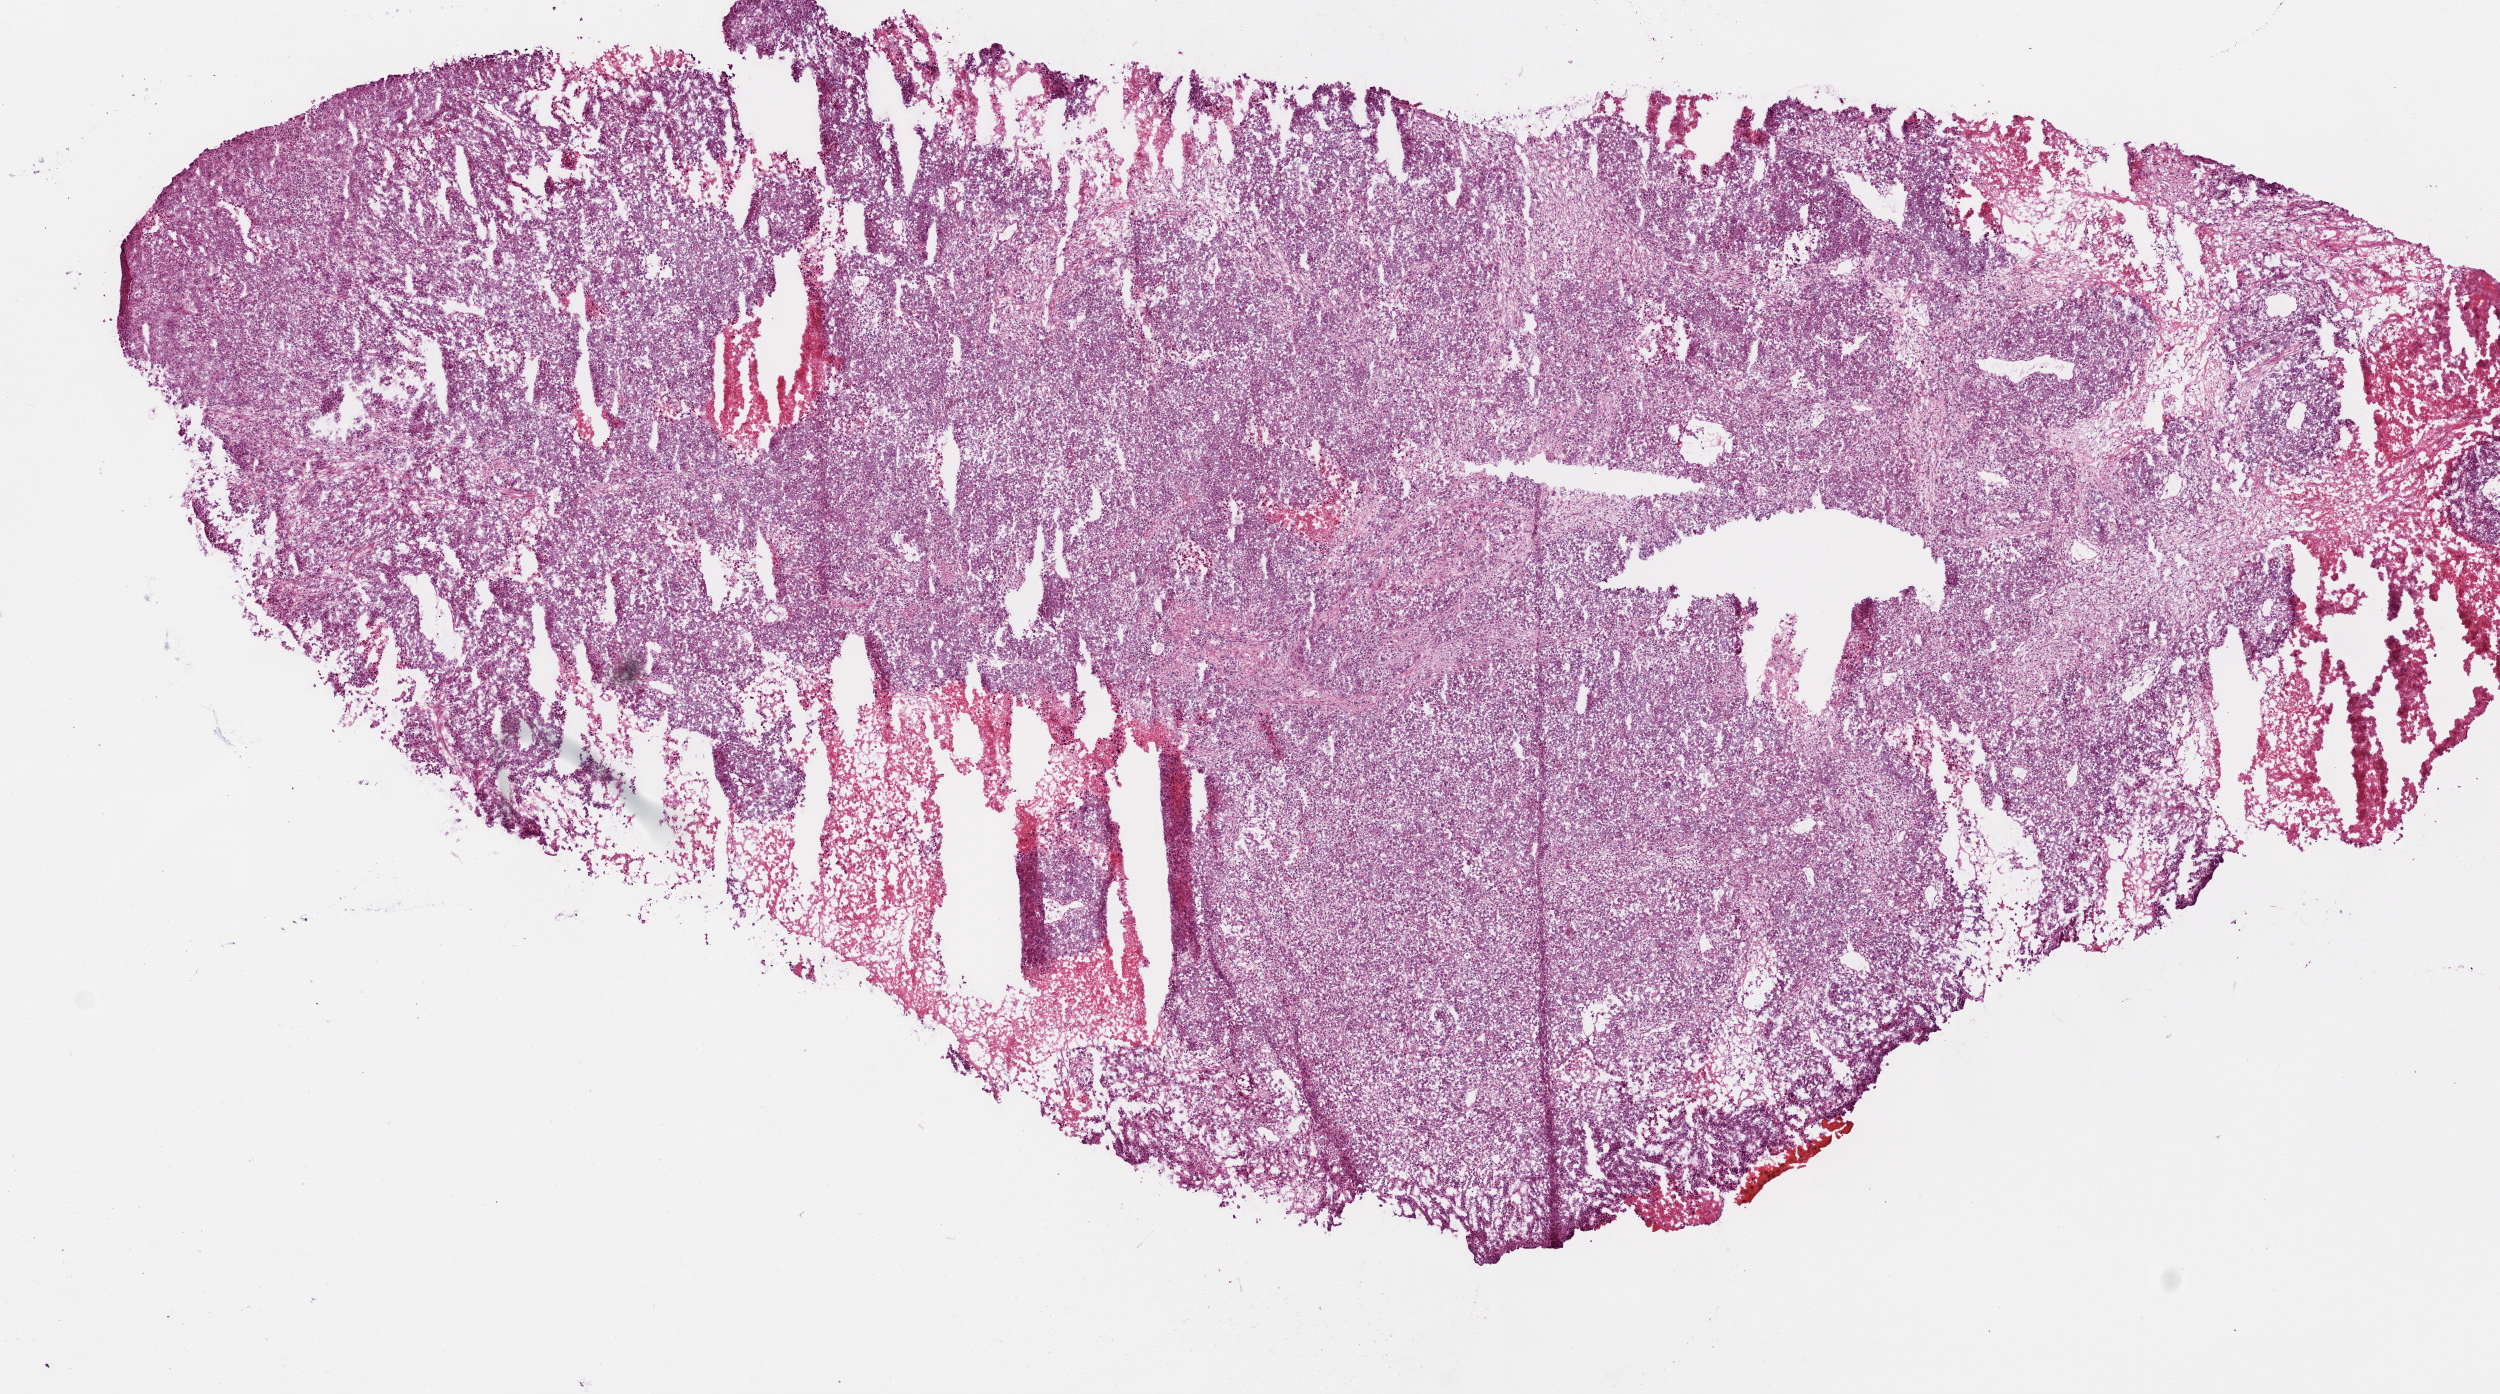
Digitized Hematoxylin and eosin (H&E) stained tissue section (whole slide), shown as a low-resolution overview of the whole scanned area (about 10.0 x 5.6 mm, slide scanned at 20x); frozen section from the bottom of the tissue portion; lung, primary tumour sample. Female, age 65 years at initial diagnosis. Composition of this section per pathologist review: tumour cells 75%, tumour nuclei 80%, normal cells 0%, stromal cells 10%, necrosis 15%.
- laterality: right
- AJCC pathologic stage: IA (7th edition)
- histologic diagnosis: Squamous cell carcinoma, NOS (upper lobe, lung)